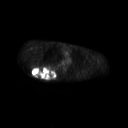
FDG PET of an extremity soft-tissue mass (from a PET/CT study), one axial slice; position 190 of 267 along the scan axis; 128 × 128 image matrix, field of view 700 × 700 mm. Patient: male, 61 years. From the clinical record (not read from this slice): histological type: pleiomorphic spindle cell undifferentiated; grade: high; site of the primary tumour: right parascapusular.
Structures marked on this image (expert contour drawn on MRI and transferred to this co-registered scan by the dataset authors):
- gross tumour volume including surrounding oedema: box from (x=32, y=65) to (x=59, y=79) px
- gross tumour volume (mass): (x=32, y=65)–(x=55, y=78)